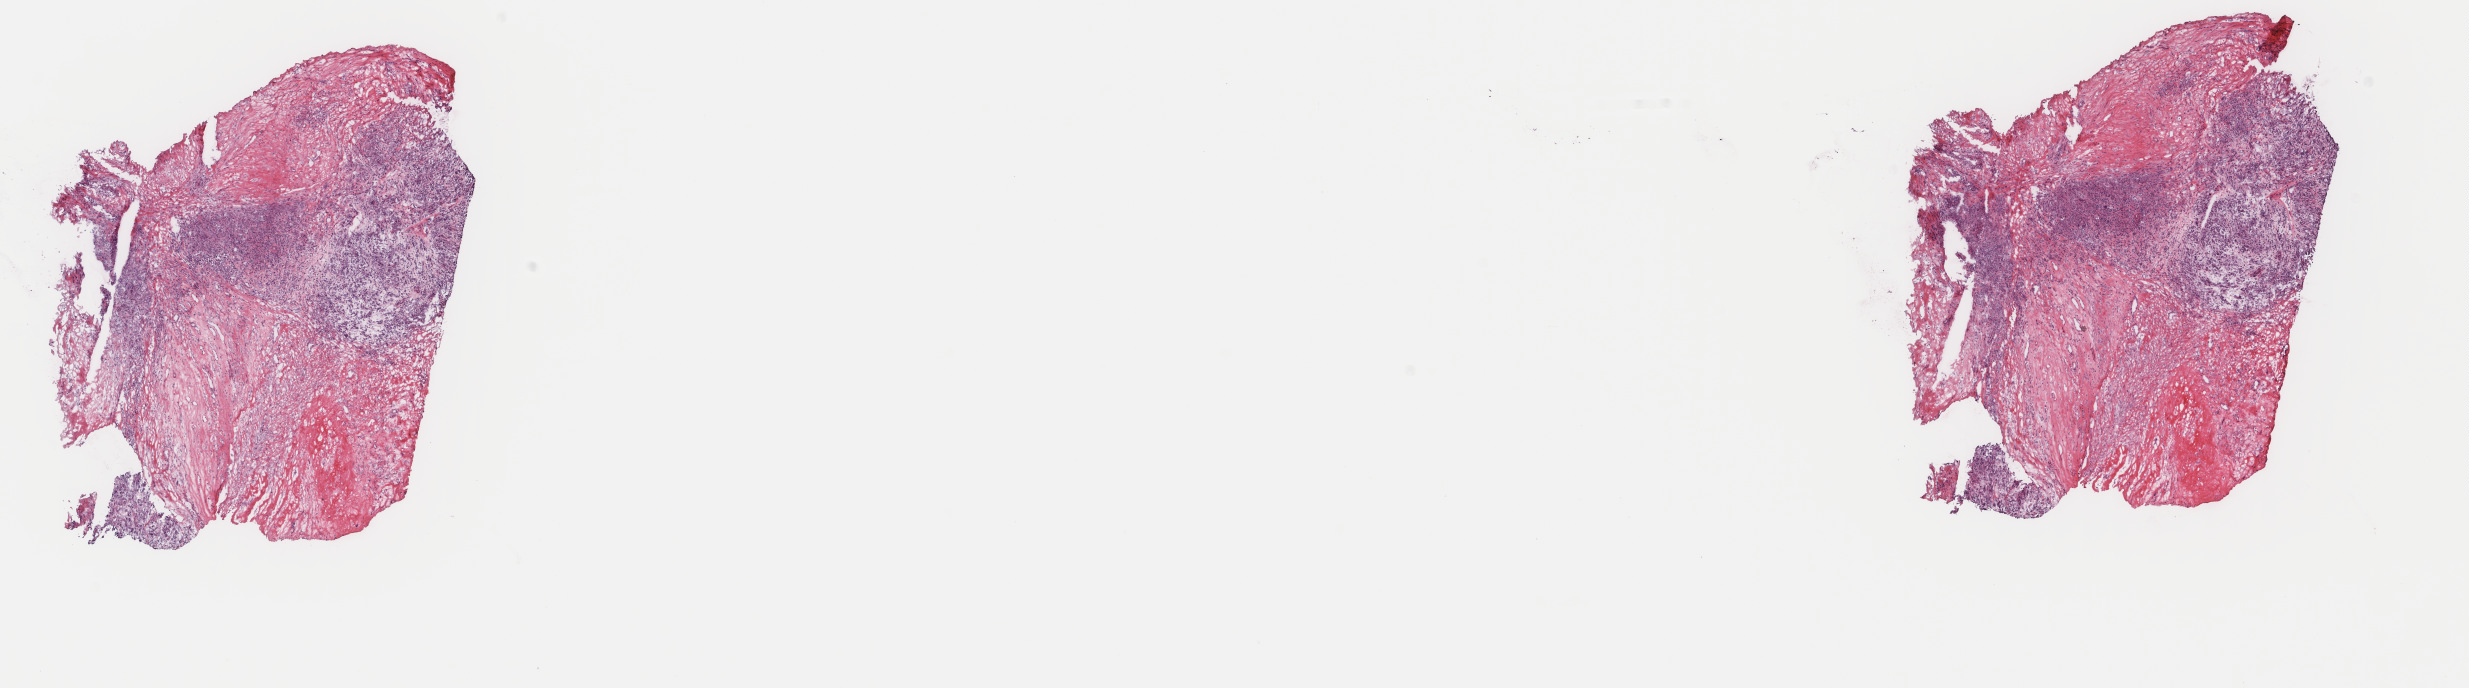
H&E-stained whole-slide image — whole scanned area (about 19.6 x 5.5 mm, slide scanned at 40x) shown as a low-resolution overview. Frozen section from the top of the tissue portion. Primary tumour sample from the connective, subcutaneous and other soft tissues. Patient: male, age at initial diagnosis 68 years. Pathologist review of this section (percent, as recorded): tumour cells 60%, tumour nuclei 60%, normal cells 0%, stromal cells 40%, necrosis 0%. Inflammatory infiltration, as recorded: lymphocyte infiltration 0%, monocyte infiltration 0%, neutrophil infiltration 0%.
• diagnosis: Undifferentiated sarcoma